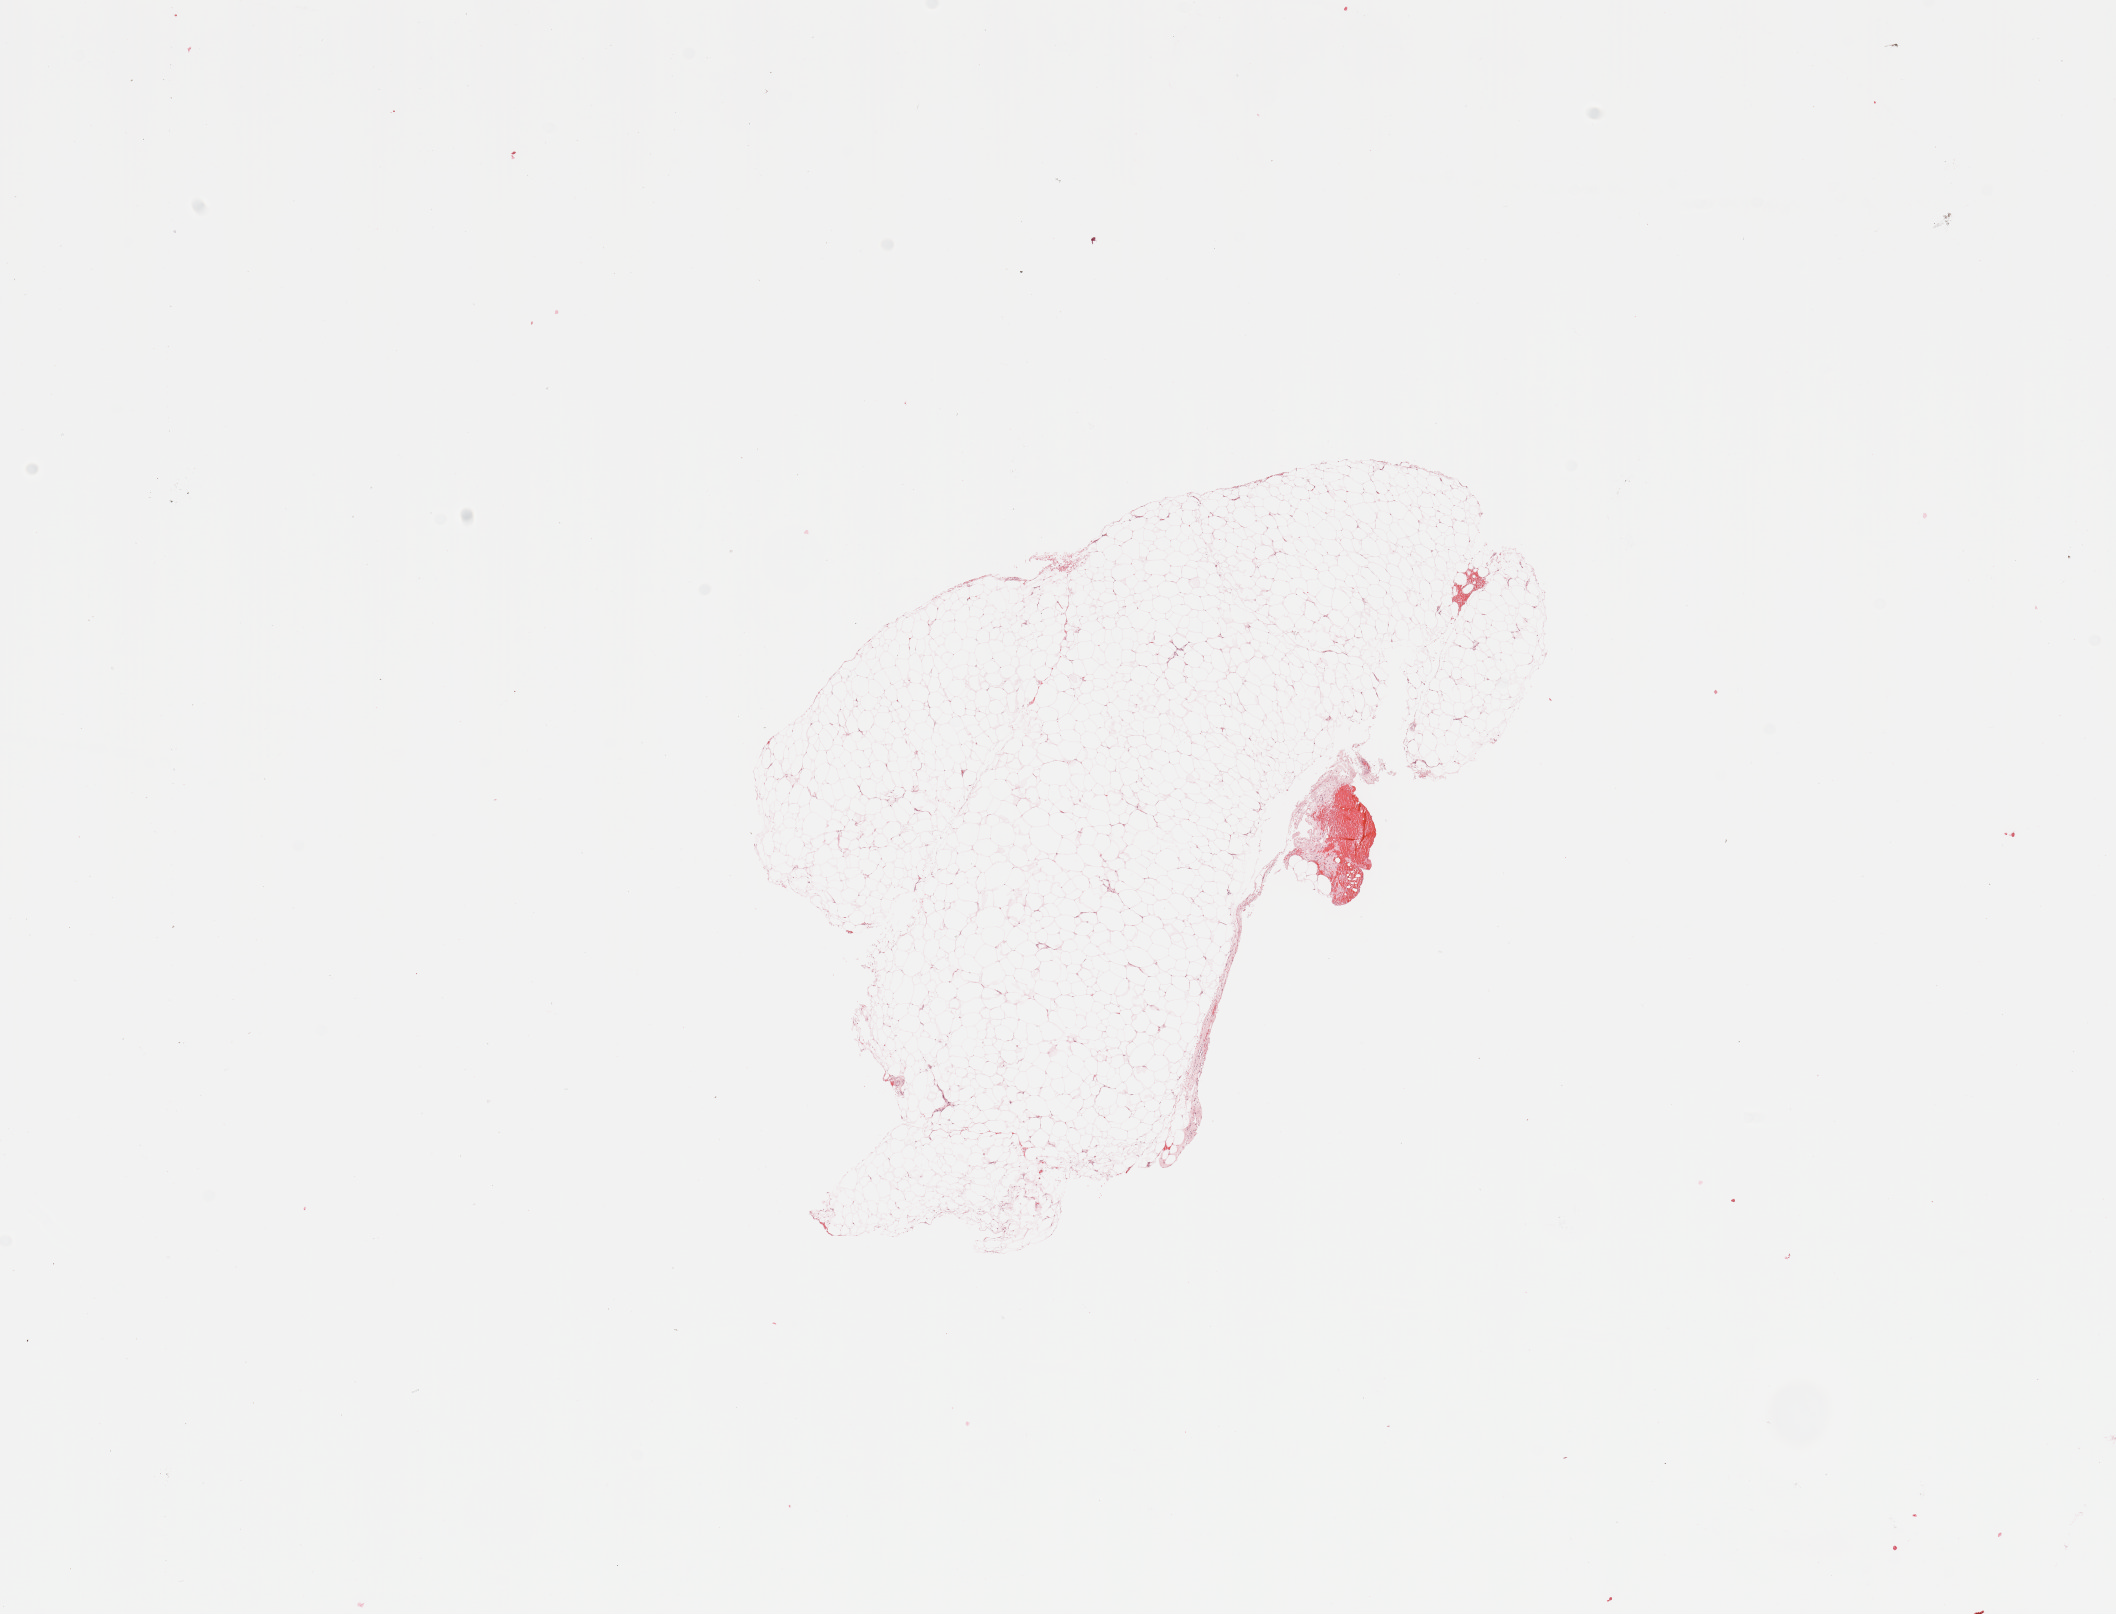
Hematoxylin and eosin (H&E) stained whole-slide image, shown as a low-resolution overview of the whole scanned area (about 16.7 x 12.8 mm), kidney, normal (non-tumour) tissue. 51-year-old male patient.
• this section: normal (non-tumour) tissue from the same patient
• patient diagnosis: Renal cell carcinoma, NOS